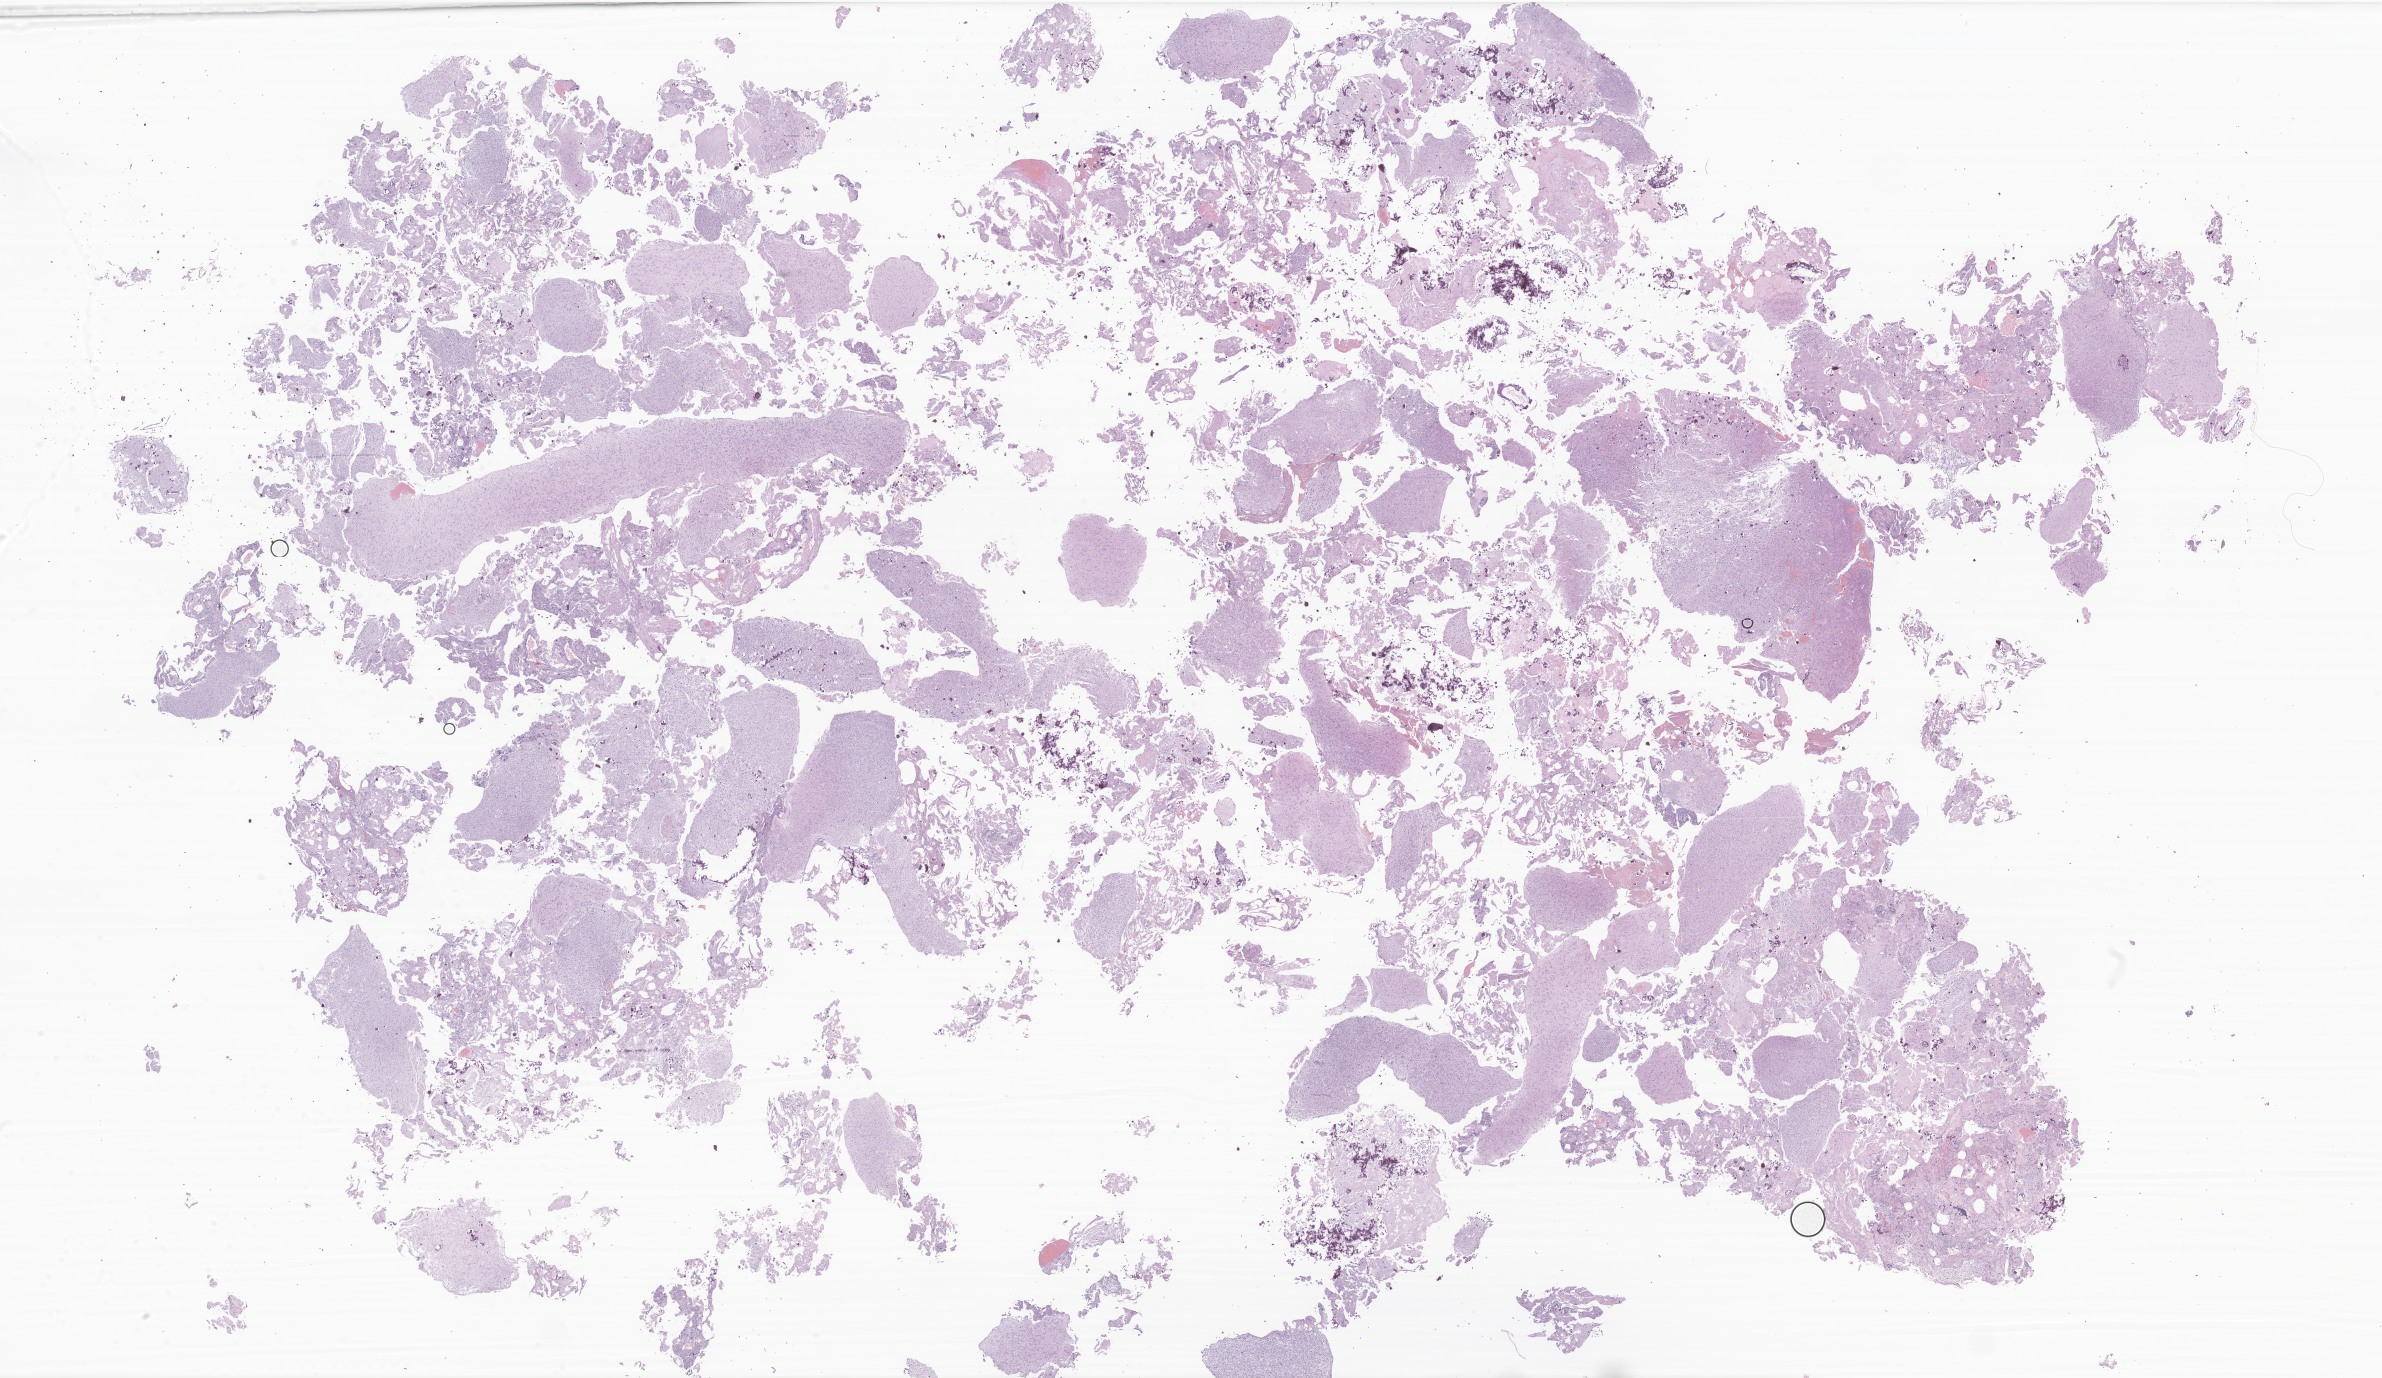
Whole-slide image, hematoxylin and eosin (H&E) stain of tumor tissue from the cerebral ventricle — low-resolution overview of the scanned area, about 40.2 x 23.2 mm; formalin-fixed, paraffin-embedded (FFPE) tissue. Female patient, age 139 months (11 years 7 months).
* diagnosis: Glioma, malignant